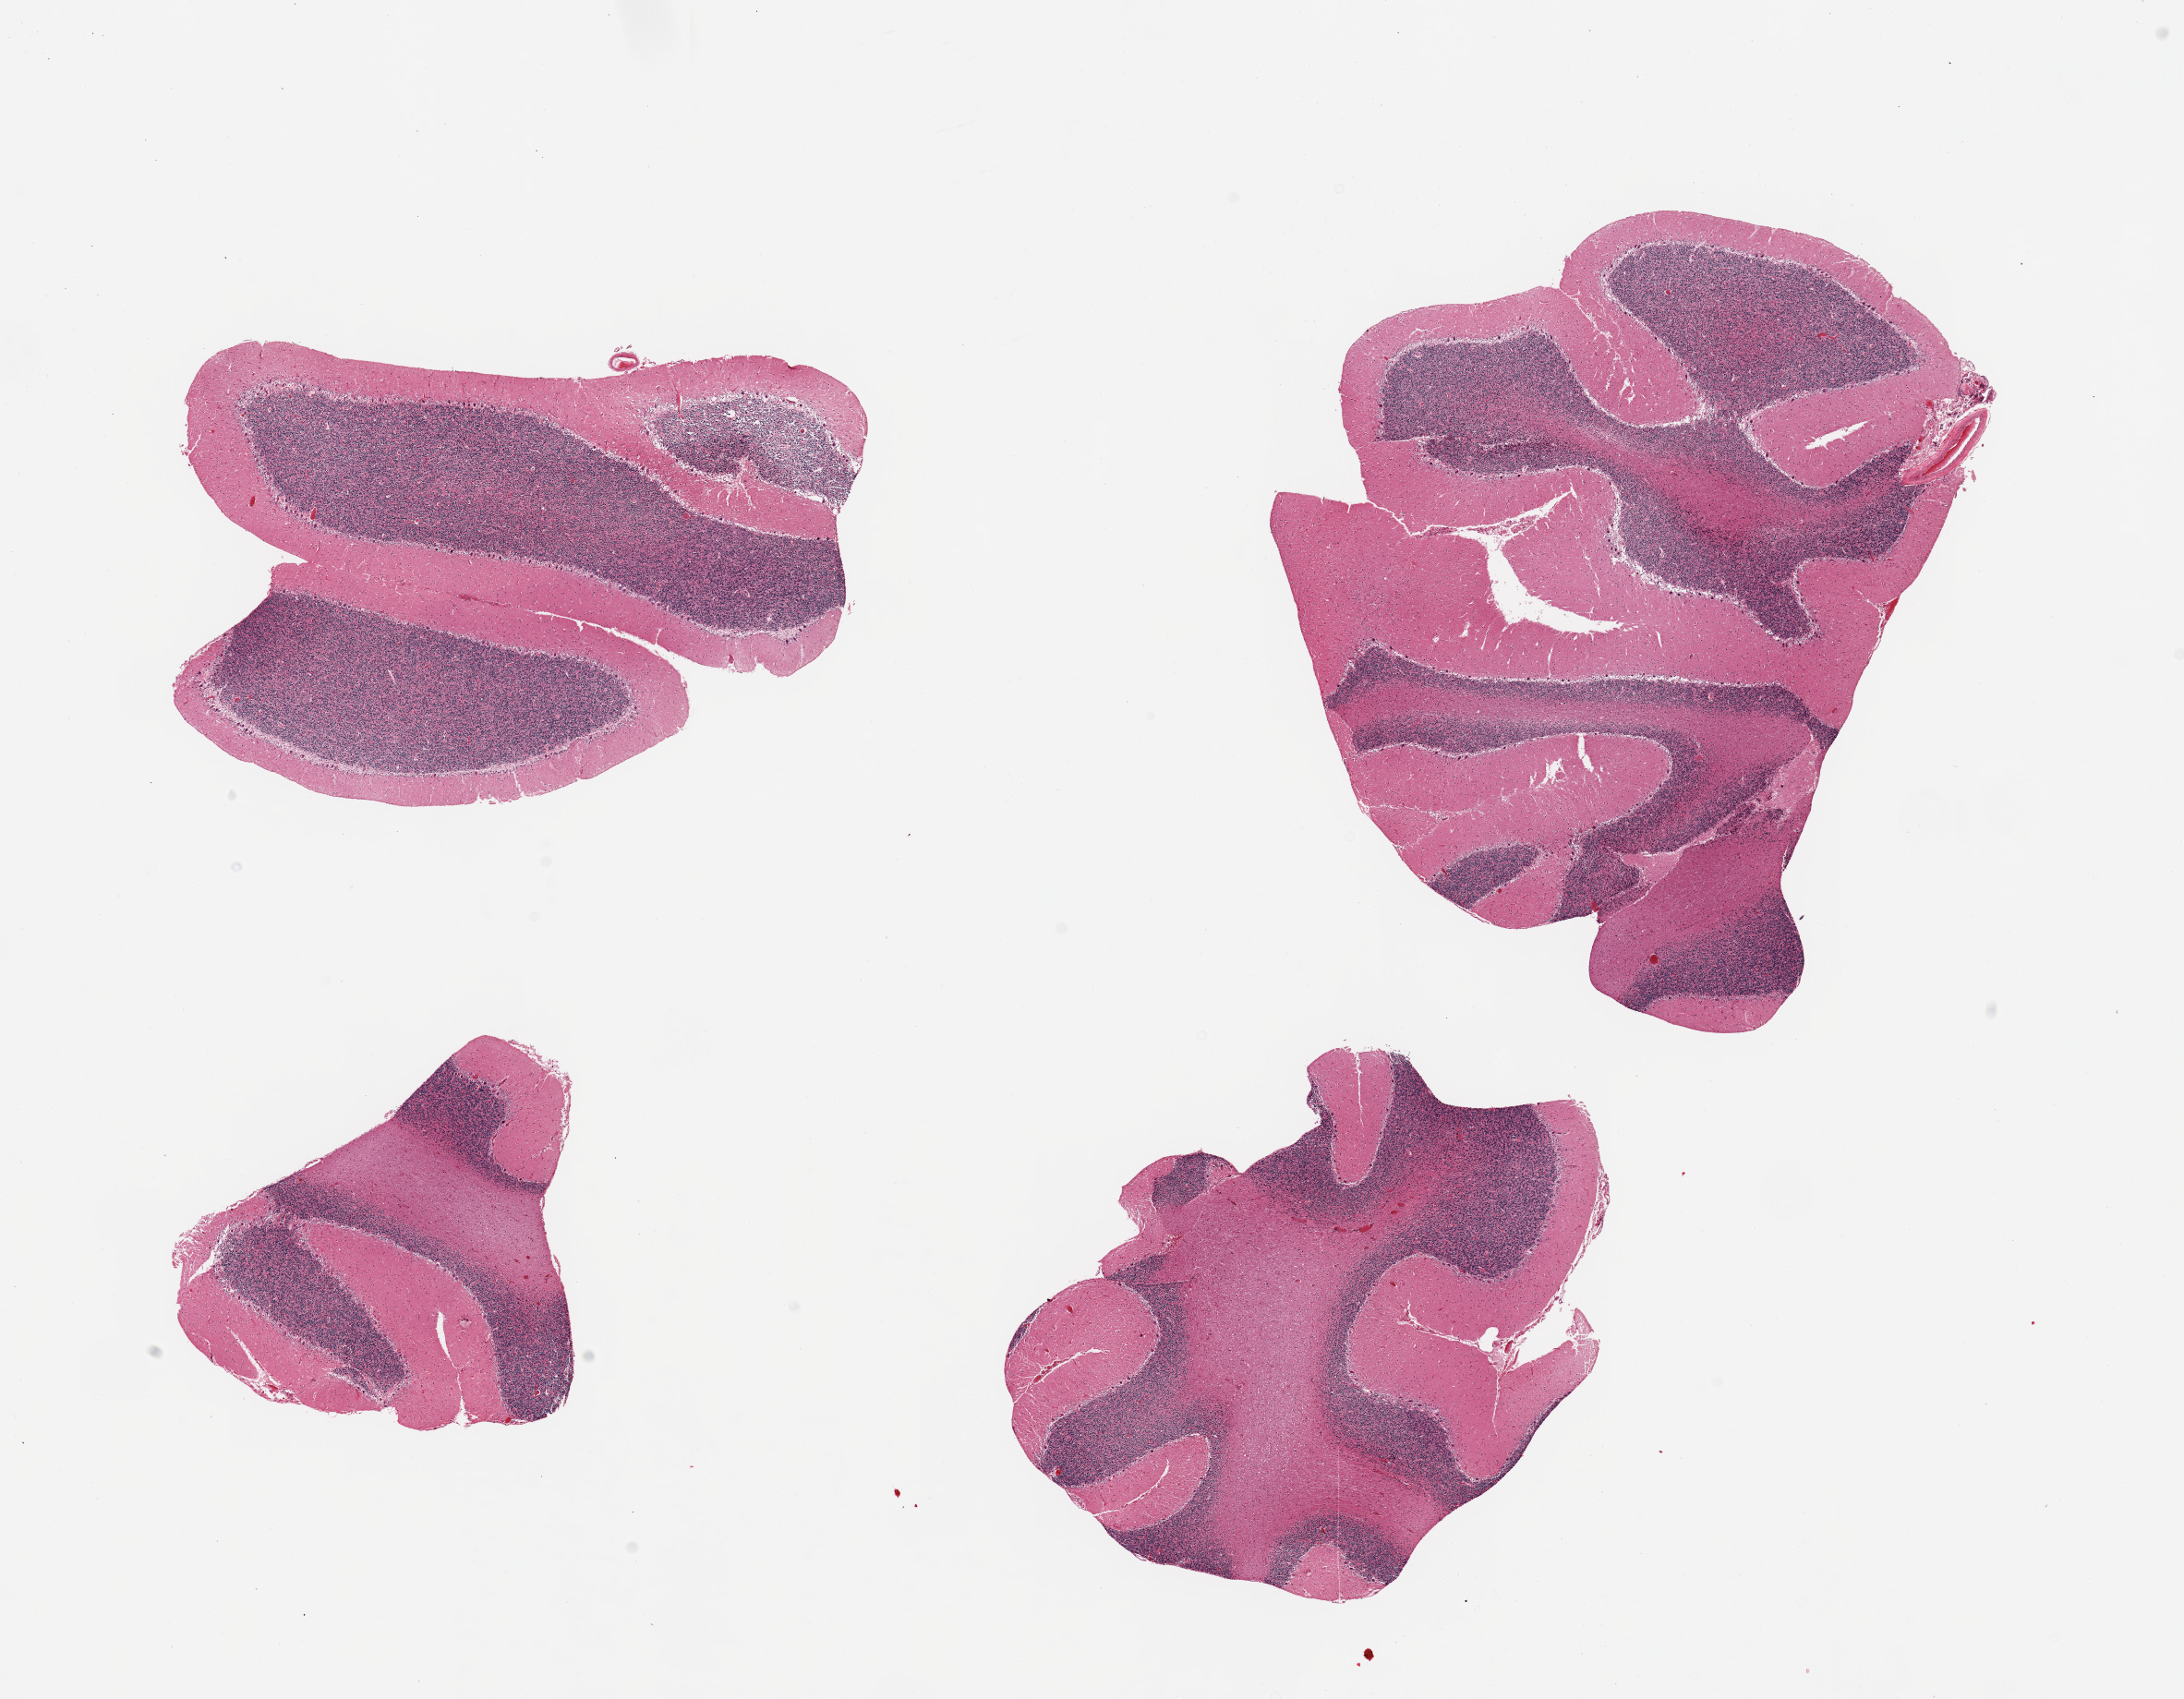
Whole-slide image, H&E stain, brightfield — a low-resolution overview of the entire scanned area, about 18.7 x 14.6 mm, PAXgene-fixed, paraffin-embedded tissue, target tissue: cerebellum, donor tissue sample. Female donor.
Reviewer comment on this tissue sample: 4 pieces.